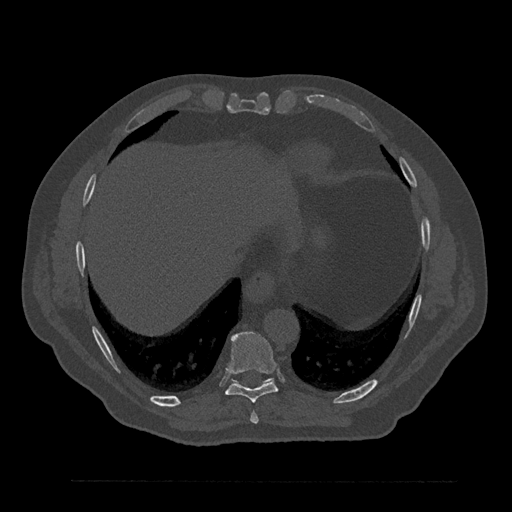
CT including the spine, one axial slice; reconstruction kernel Br40s/3; 120 kVp; bone window (W 1800 / L 400 HU); 0.5 mm slice thickness; 512 × 512 image matrix, field of view 430 × 430 mm. Male patient, age 61 years. From the clinical record (not read from this slice): primary cancer: prostate.
Outlined on this slice (semi-automatically segmented with operator editing):
- T10 vertebra: bounding box [x1, y1, x2, y2] px = [232, 379, 272, 384]
- T8 vertebra: [250, 412, 259, 424]
- T9 vertebra: [225, 332, 278, 403]